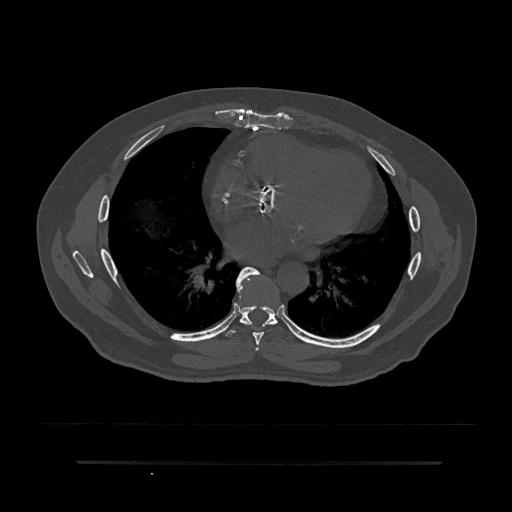
CT including the spine, one axial slice. Slice 454 of 797 in the series (ordered by position). Reconstruction kernel Br40s/3. 120 kVp. Bone window (W 1800 / L 400 HU). 0.5 mm slice thickness. 512 × 512 image matrix, field of view 464 × 464 mm. Patient: male, 59 years. From the clinical record (not read from this slice): primary cancer: bile ducts; vertebrae with lytic lesions (as recorded): T10.
Annotated regions visible in this slice (semi-automatic segmentation, software-assisted and operator-edited):
- T6 vertebra: bounding box (x1, y1, x2, y2) in pixels: (255, 347, 259, 351)
- T7 vertebra: (236, 266, 275, 345)
- T8 vertebra: (223, 272, 297, 337)